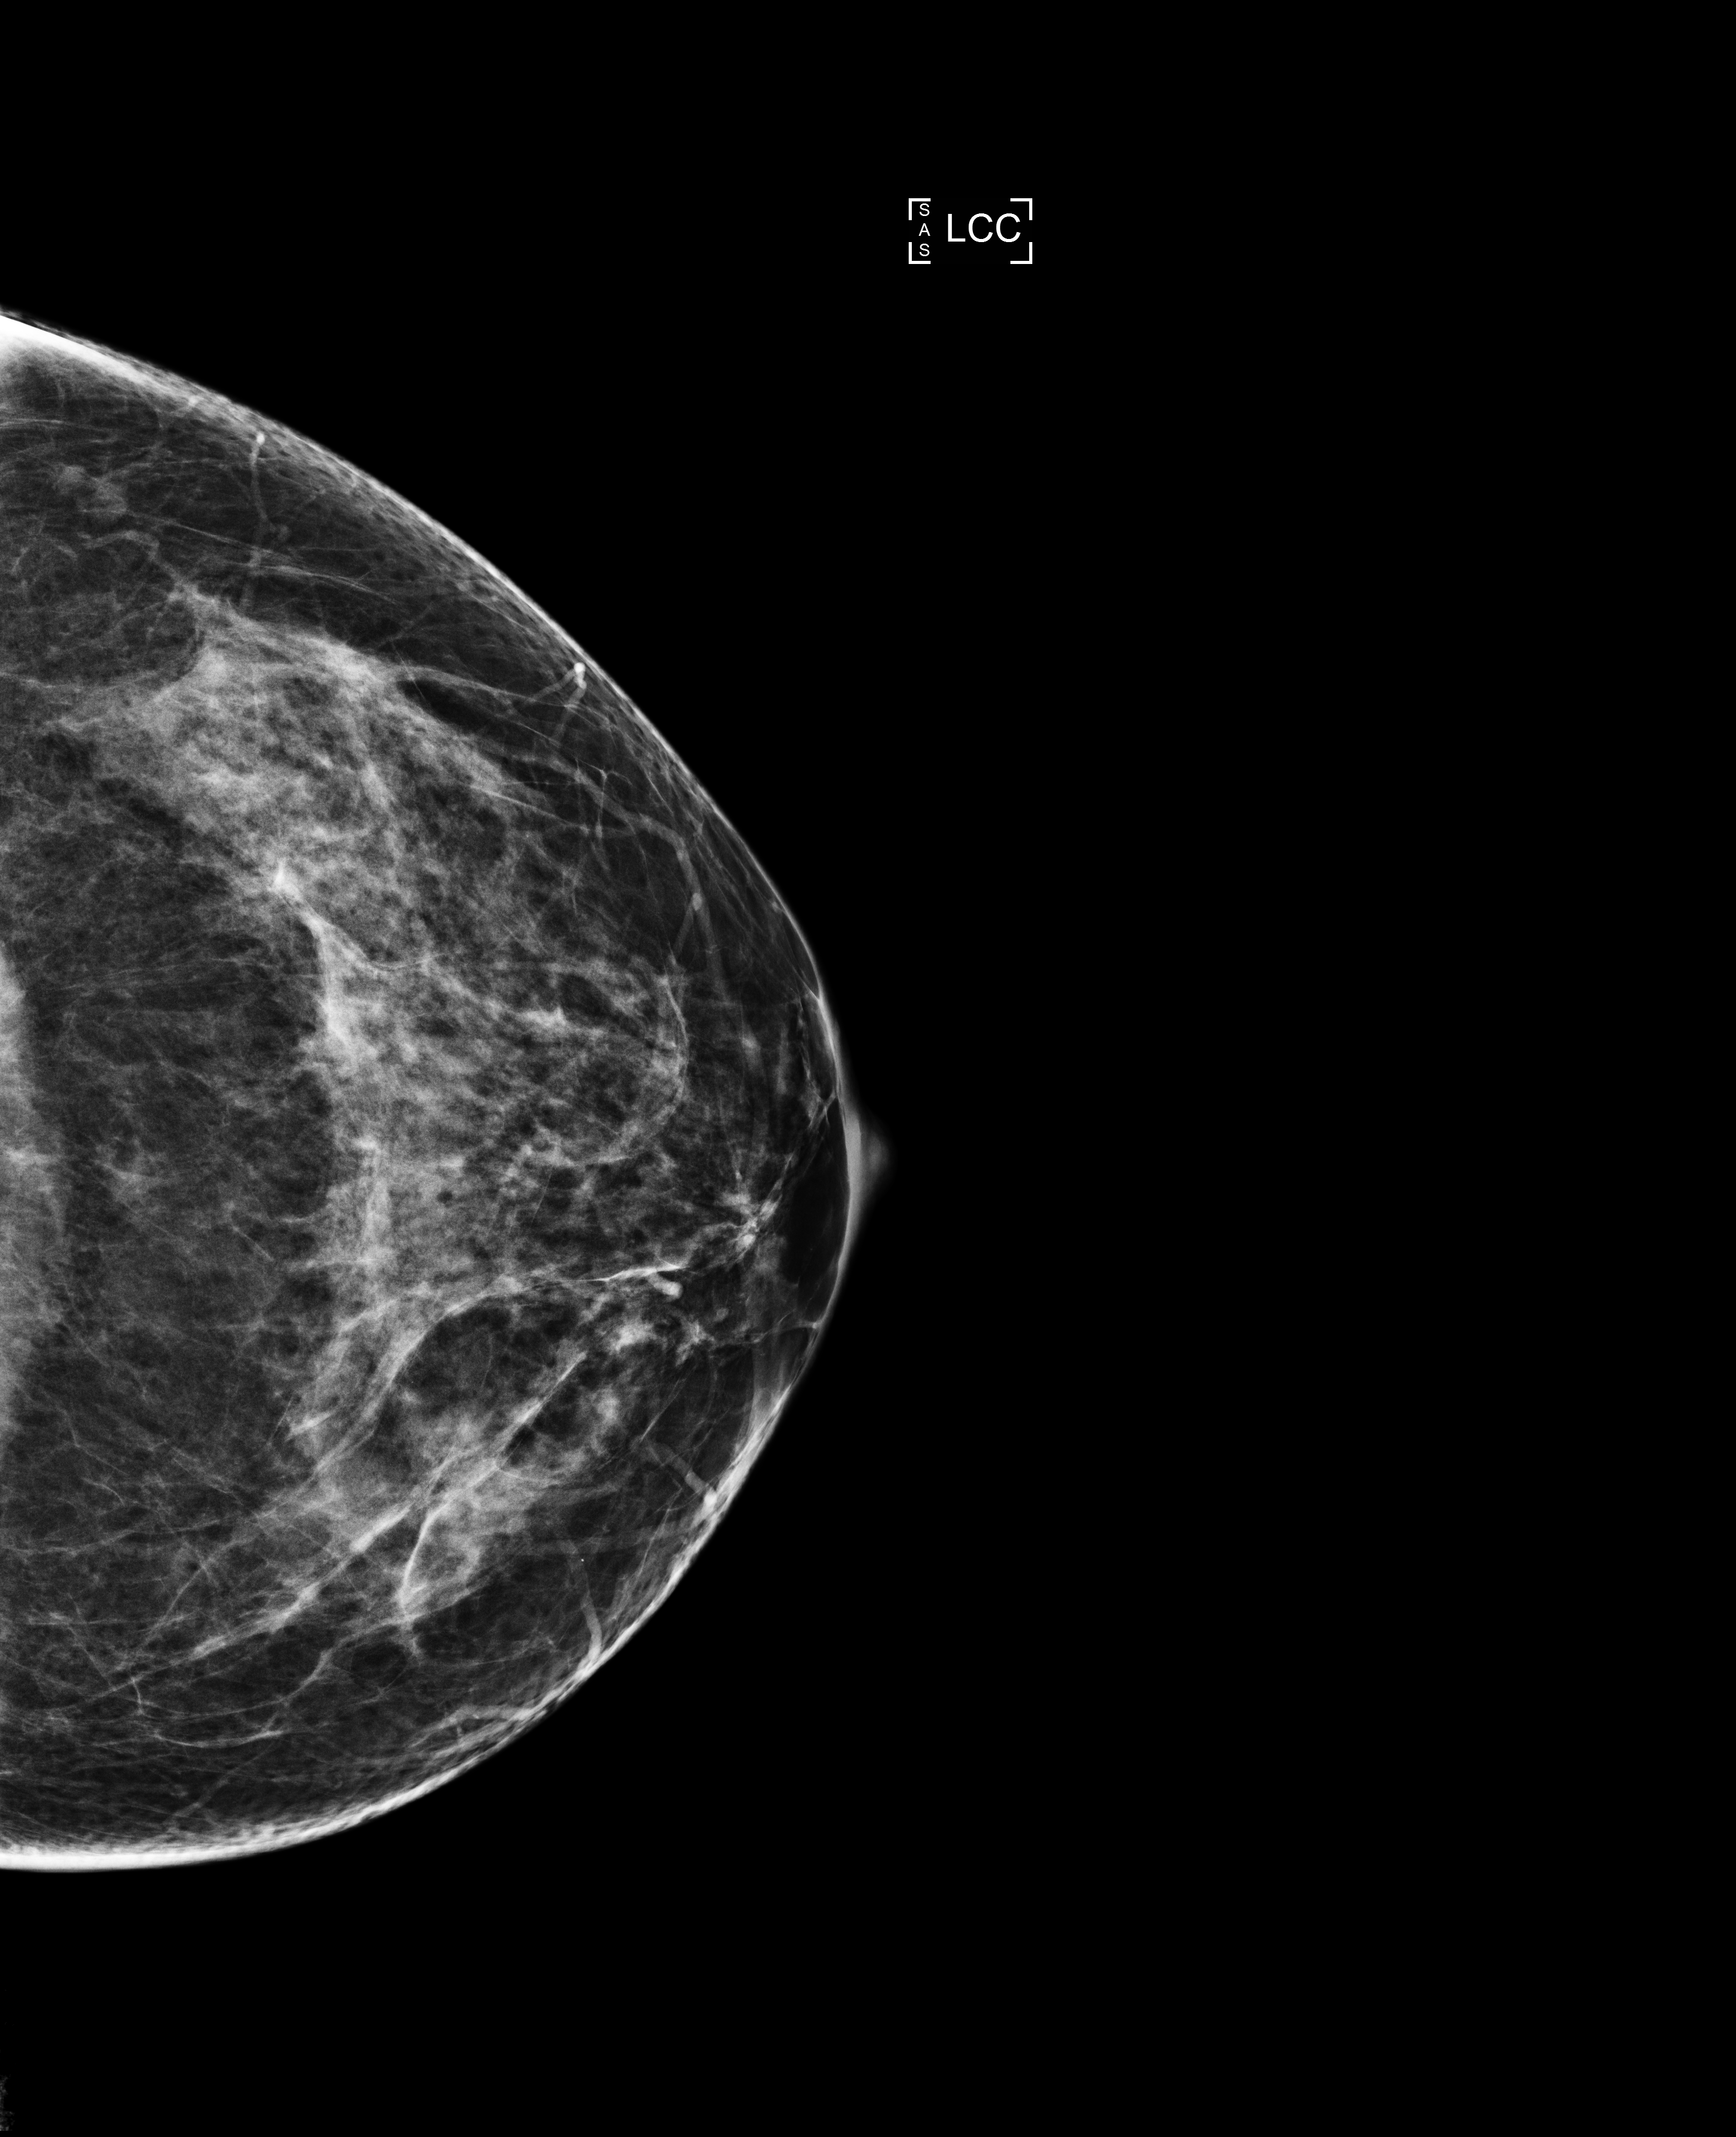
Screening examination; compressed breast thickness 60 mm; system: Selenia Dimensions. Patient aged 45 years (female).
Image type: full-field digital mammogram. Breast: left. Projection: cranio-caudal projection.